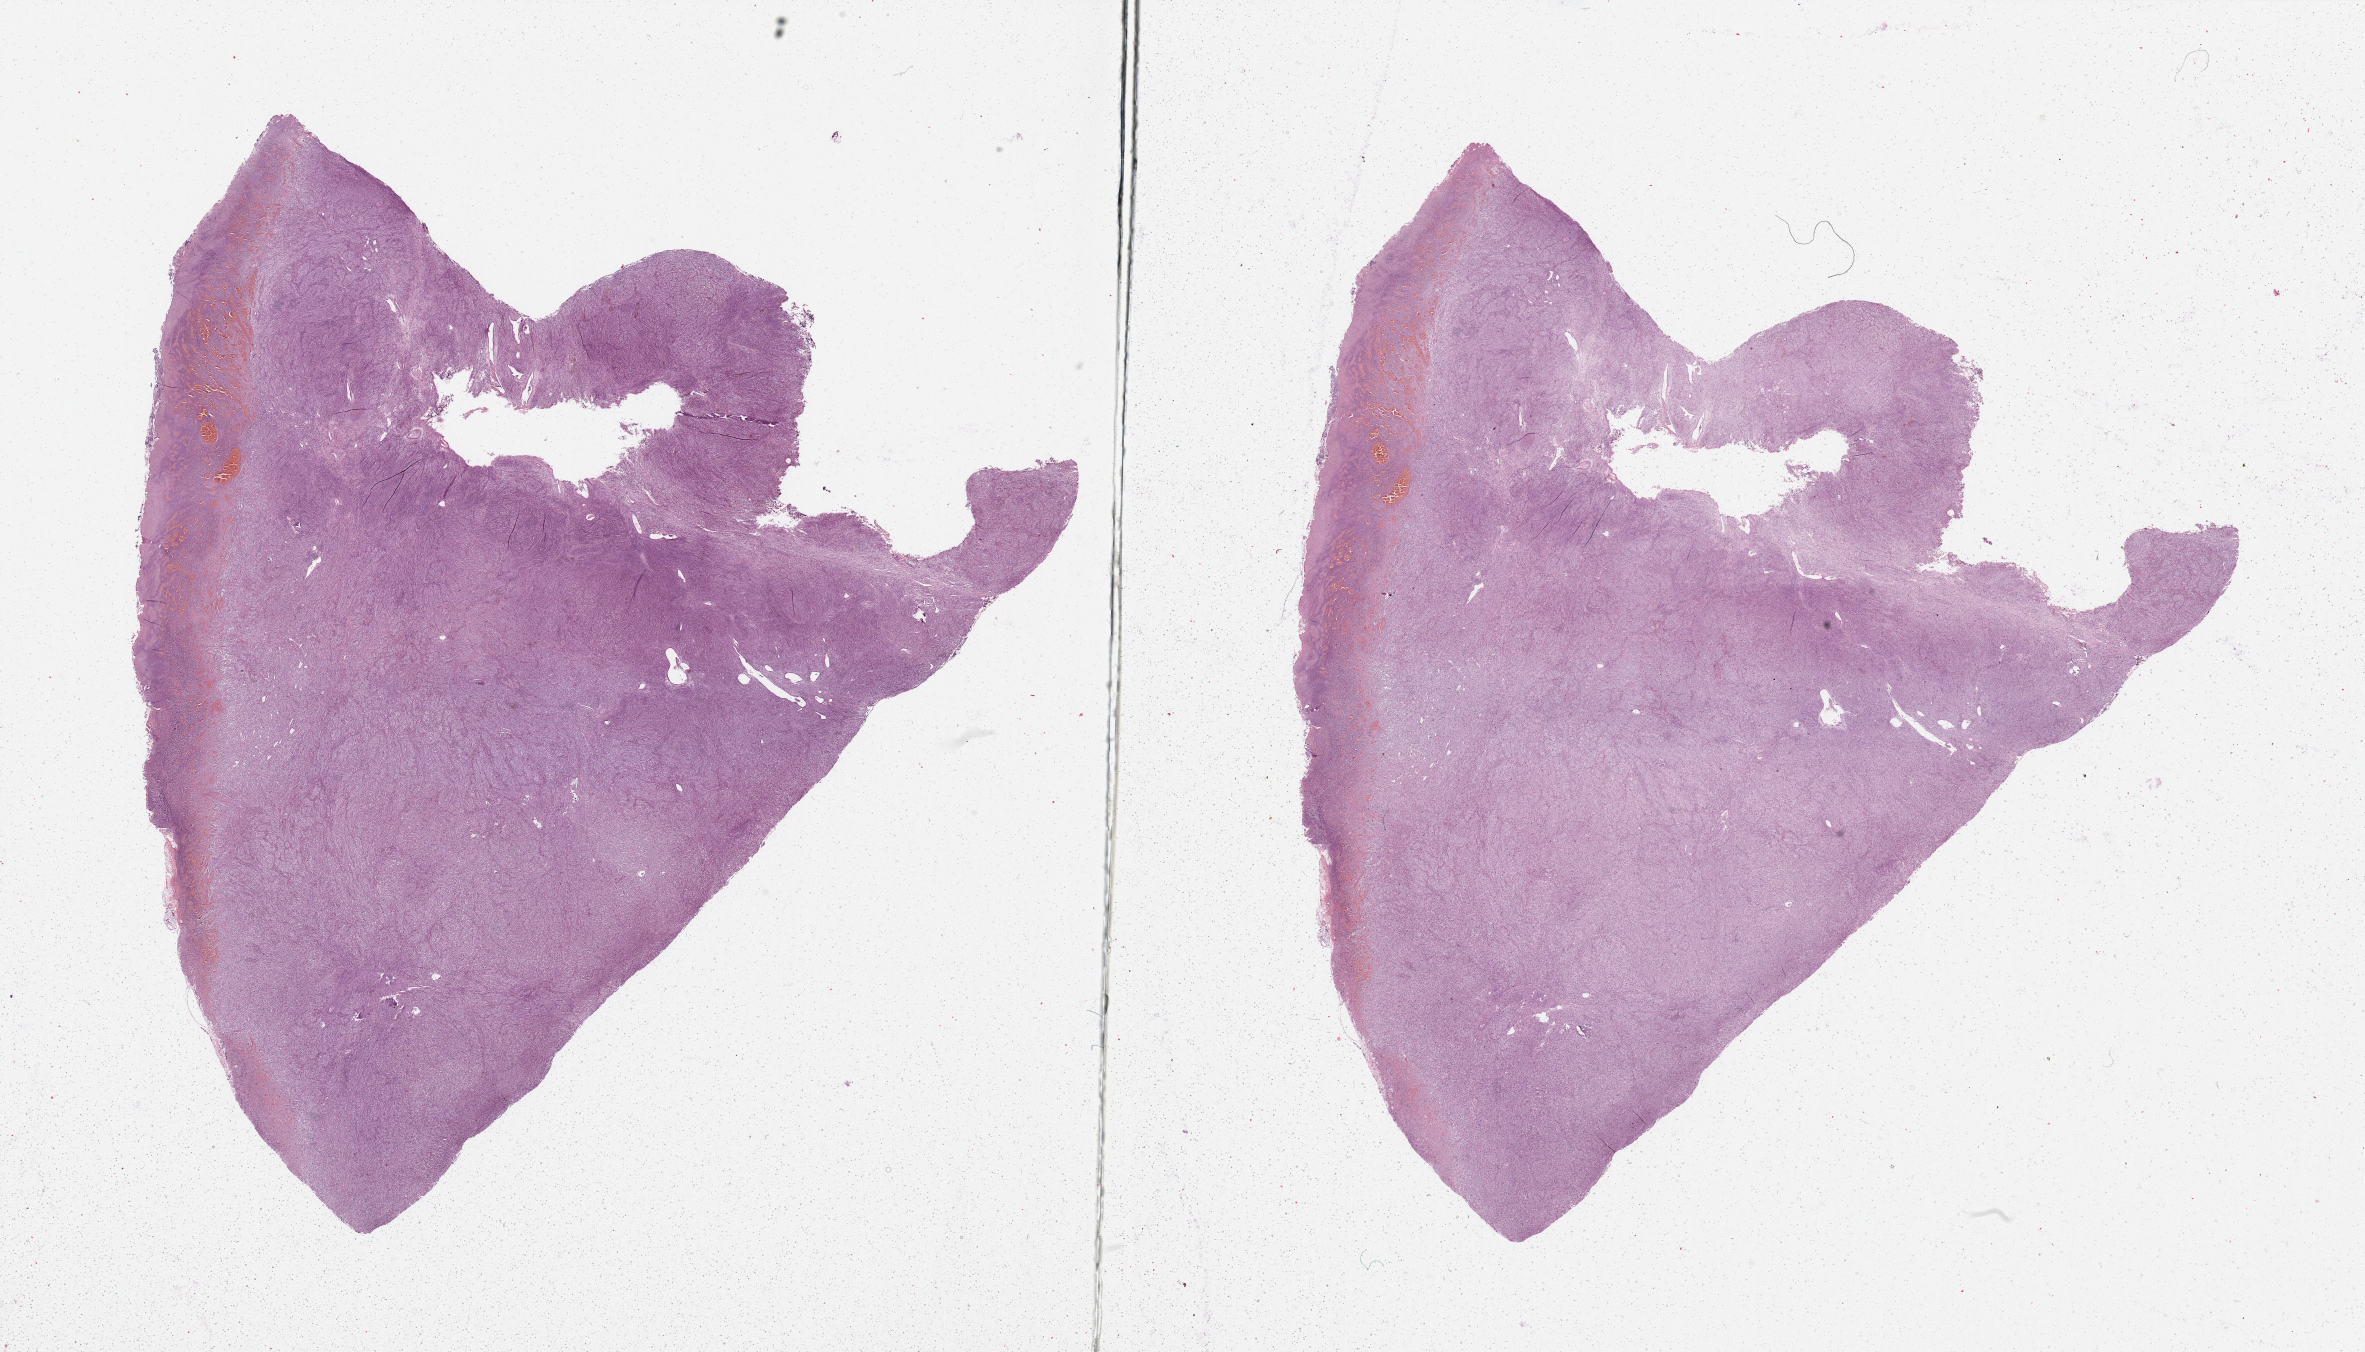
Digitized H&E-stained tissue section (whole slide) — shown as a low-resolution overview of the whole scanned area (about 37.4 x 21.4 mm), melanoma tumour tissue; sampled site not recorded. Patient: male, age 74 years.
Diagnosis: Malignant melanoma, NOS.